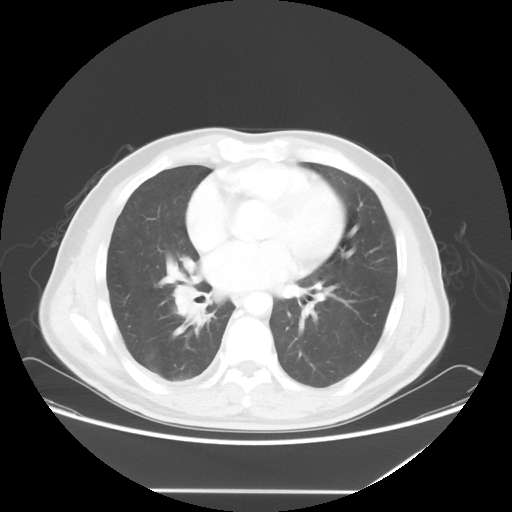
Chest CT, one axial slice; slice 27 of 60 in the series (ordered by position); 120 kVp; lung window (W 1500 / L -600 HU); 512 × 512 image matrix, field of view 419 × 419 mm. Patient: male, 48 years. From the clinical record (not read from this slice): clinical TNM (as recorded): T3 N3 M1a.
Structures marked on this image (bounding box drawn by a radiologist):
- lung tumour (recorded histology: squamous cell carcinoma): box from (x=169, y=282) to (x=218, y=334) px